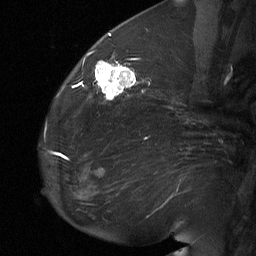
Breast MRI (dynamic contrast-enhanced), one sagittal slice; slice 25 of 64 in the series (ordered by position); dynamic contrast-enhanced study with each time point stored as its own series, time point 2 of 3 at this slice position (early post-contrast, ordered by acquisition time); 1.5 T; TE 4.8 ms, TR 27 ms; 256 × 256 image matrix, field of view 200 × 200 mm. Patient: female, 60 years. Case-level facts recorded for this patient, not image findings: setting: breast cancer imaged before/during neoadjuvant chemotherapy; receptor status: HR-positive, HER2-negative.
Outlined on this slice (semi-automatically segmented with operator editing):
- analysis volume of interest (the breast-tissue region the enhancement analysis was run in; not a lesion): box from (x=91, y=56) to (x=139, y=104) px
- tumour enhancement mask (voxels above the 90 % enhancement threshold inside the analysis volume of interest): (x=95, y=60)–(x=136, y=99)